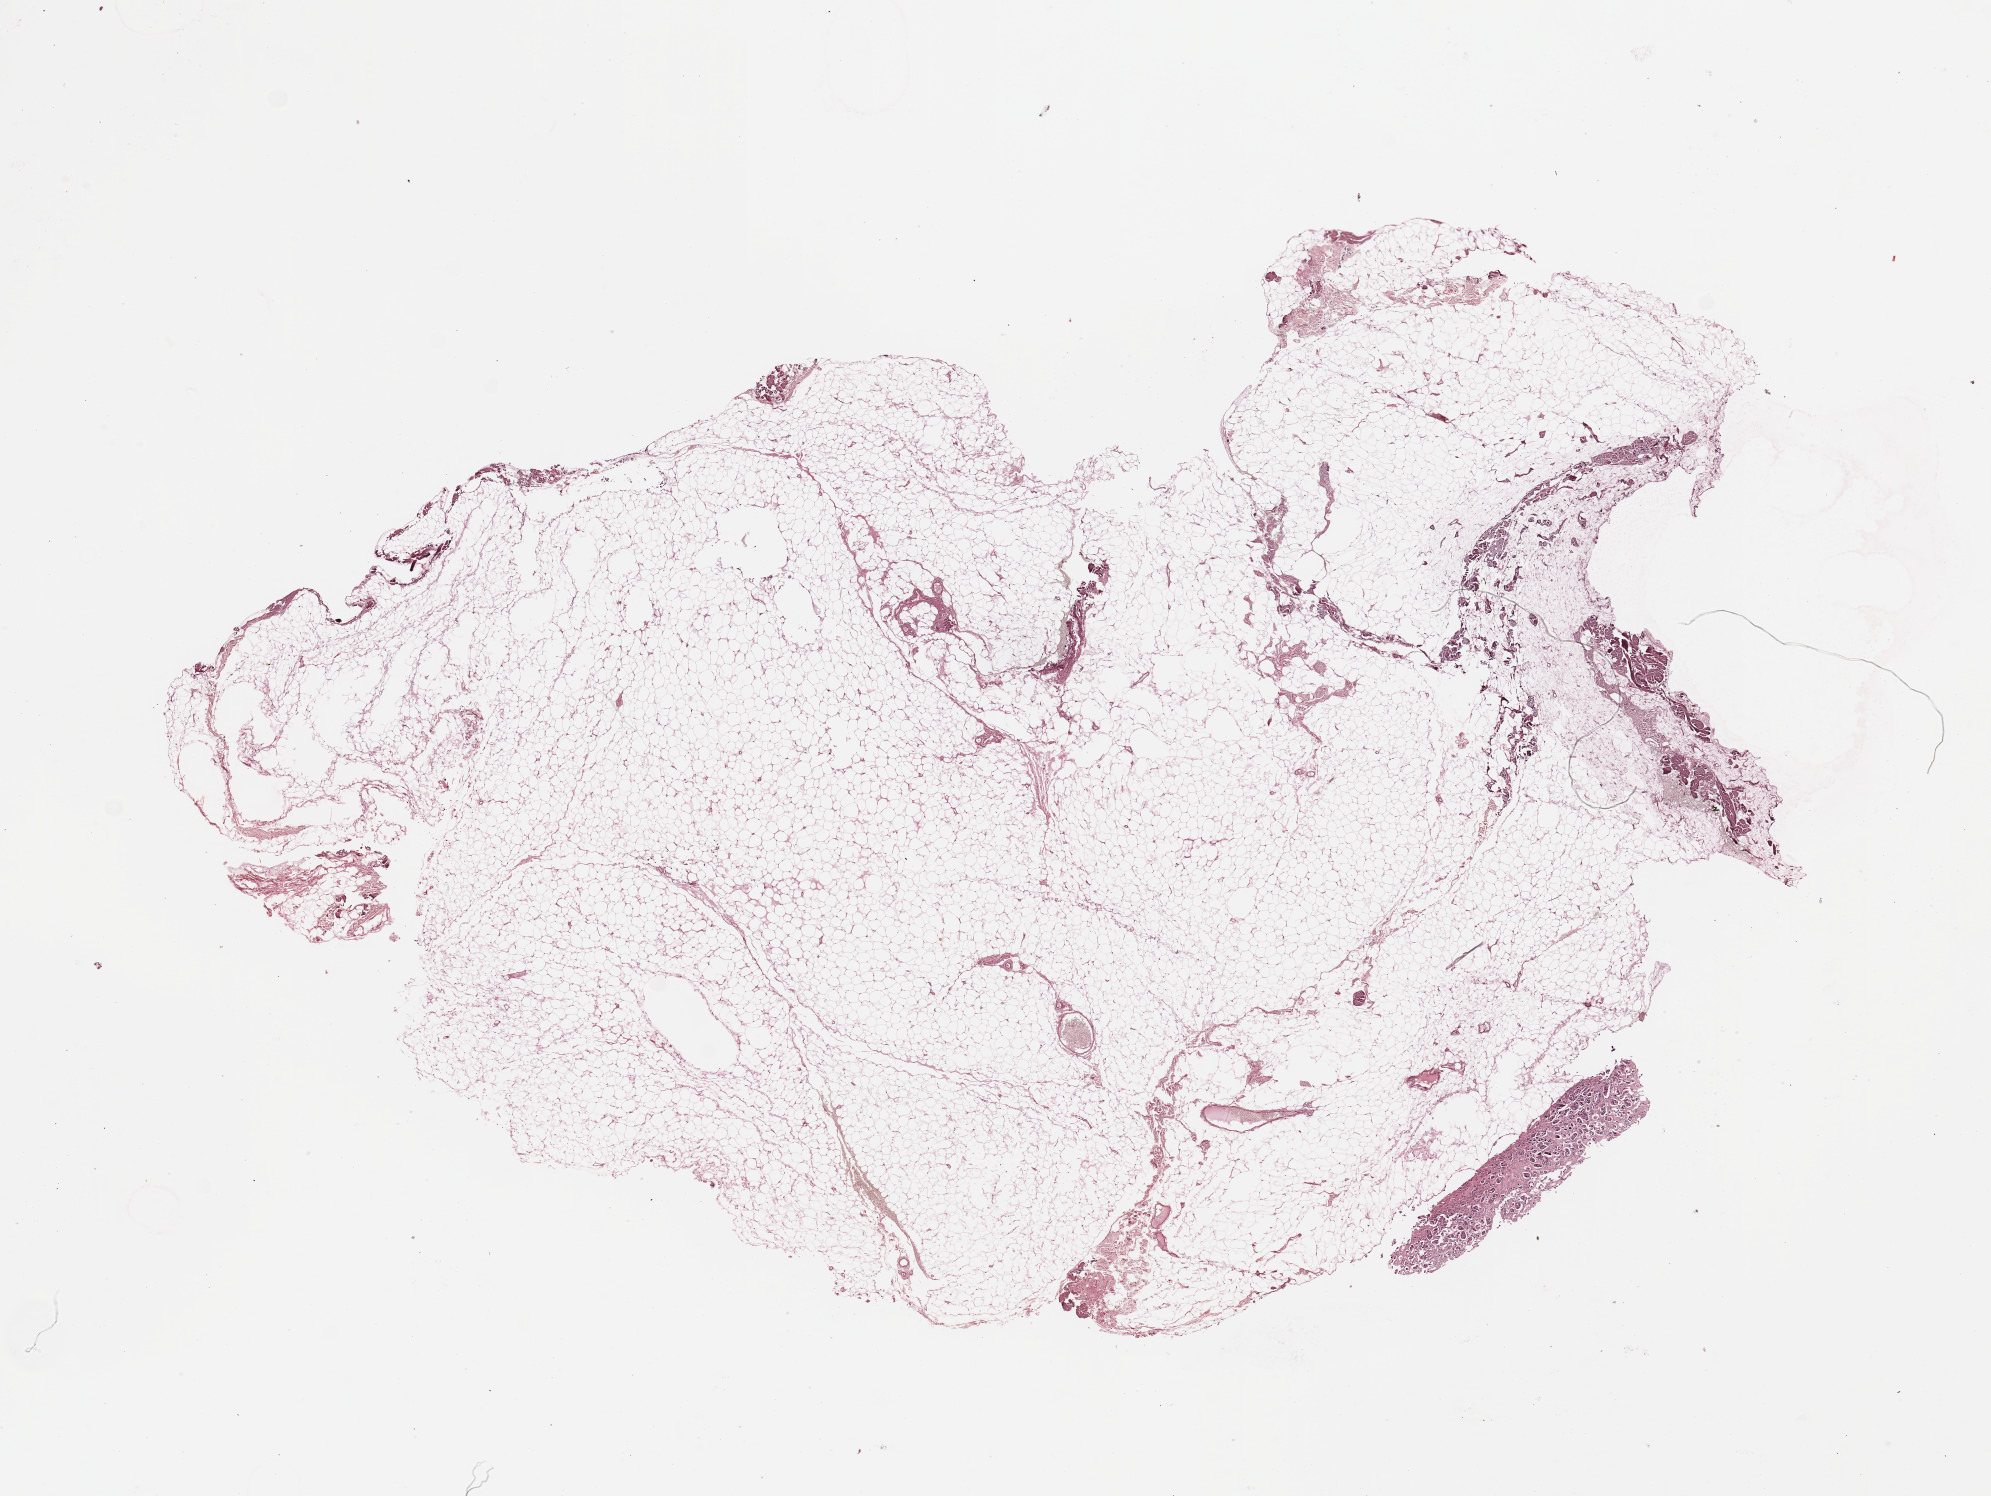
Digitized H&E tissue section (whole slide) — a low-resolution overview of the entire scanned area, about 15.8 x 11.8 mm (from a 20x scan). Normal (non-tumour) tissue (melanoma cohort); sampled site not recorded. Patient: male, age 76 years.
* this section: normal (non-tumour) tissue from the same patient
* patient diagnosis: Malignant melanoma, NOS